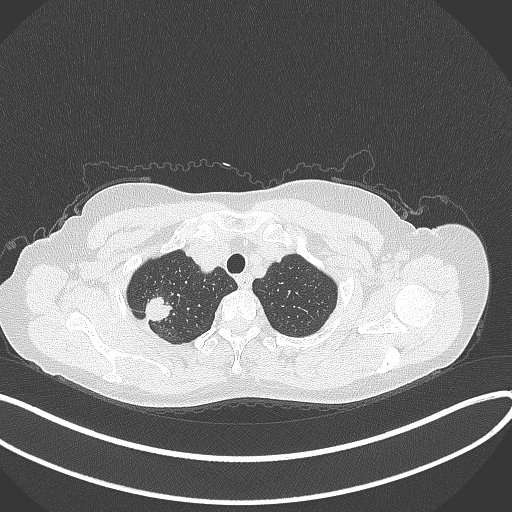
Chest CT, one axial slice; position 319 of 337 along the scan axis; reconstruction kernel B70f; 120 kVp; lung window (W 1500 / L -600 HU); 512 × 512 image matrix. Female patient, age 50 years. From the clinical record (not read from this slice): clinical TNM (as recorded): T1c N0 M0; histopathological grade: G2-3.
Annotated regions visible in this slice (bounding box drawn by a radiologist):
- lung tumour (recorded histology: adenocarcinoma): bounding box (x1, y1, x2, y2) in pixels: (137, 293, 180, 327)